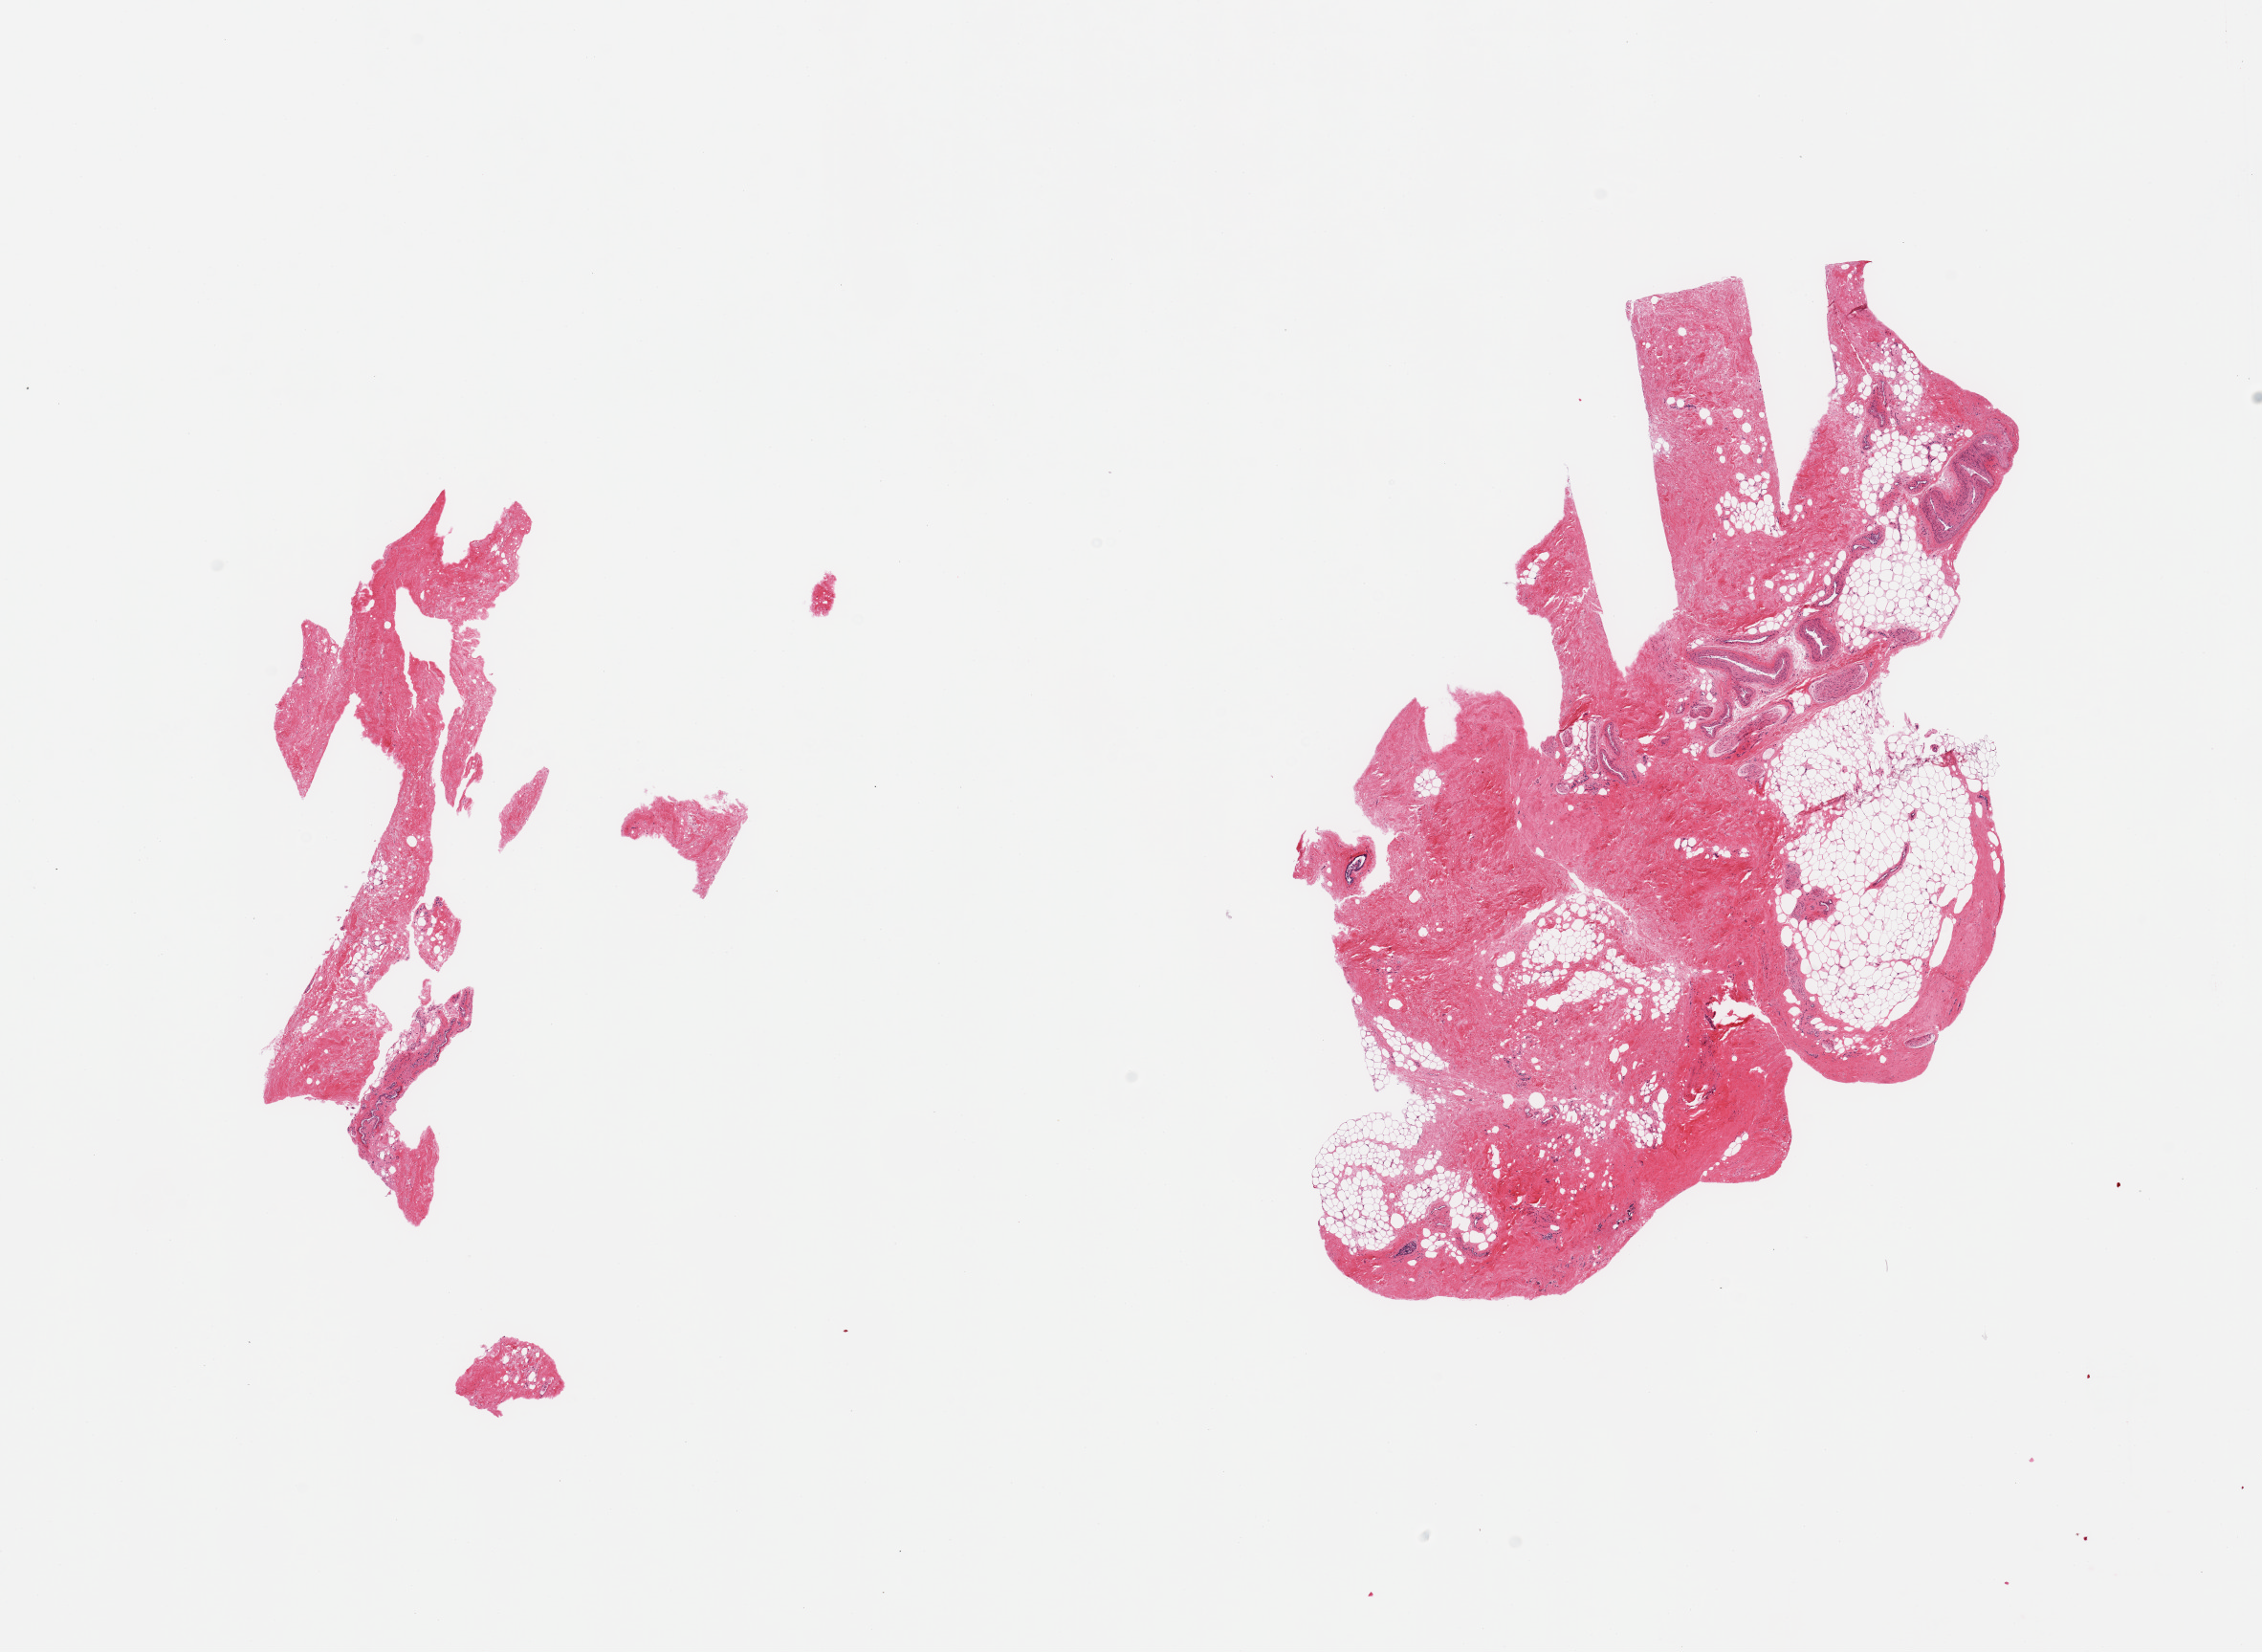
Whole-slide image, H&E stain, brightfield, a low-resolution overview of the entire scanned area, about 18.7 x 13.7 mm (from a 20x scan); PAXgene-fixed, paraffin-embedded tissue; sampled site (target tissue): breast; tissue donor sample. Male donor.
Review note (as recorded): 2 pieces, fibroadipose elements only.